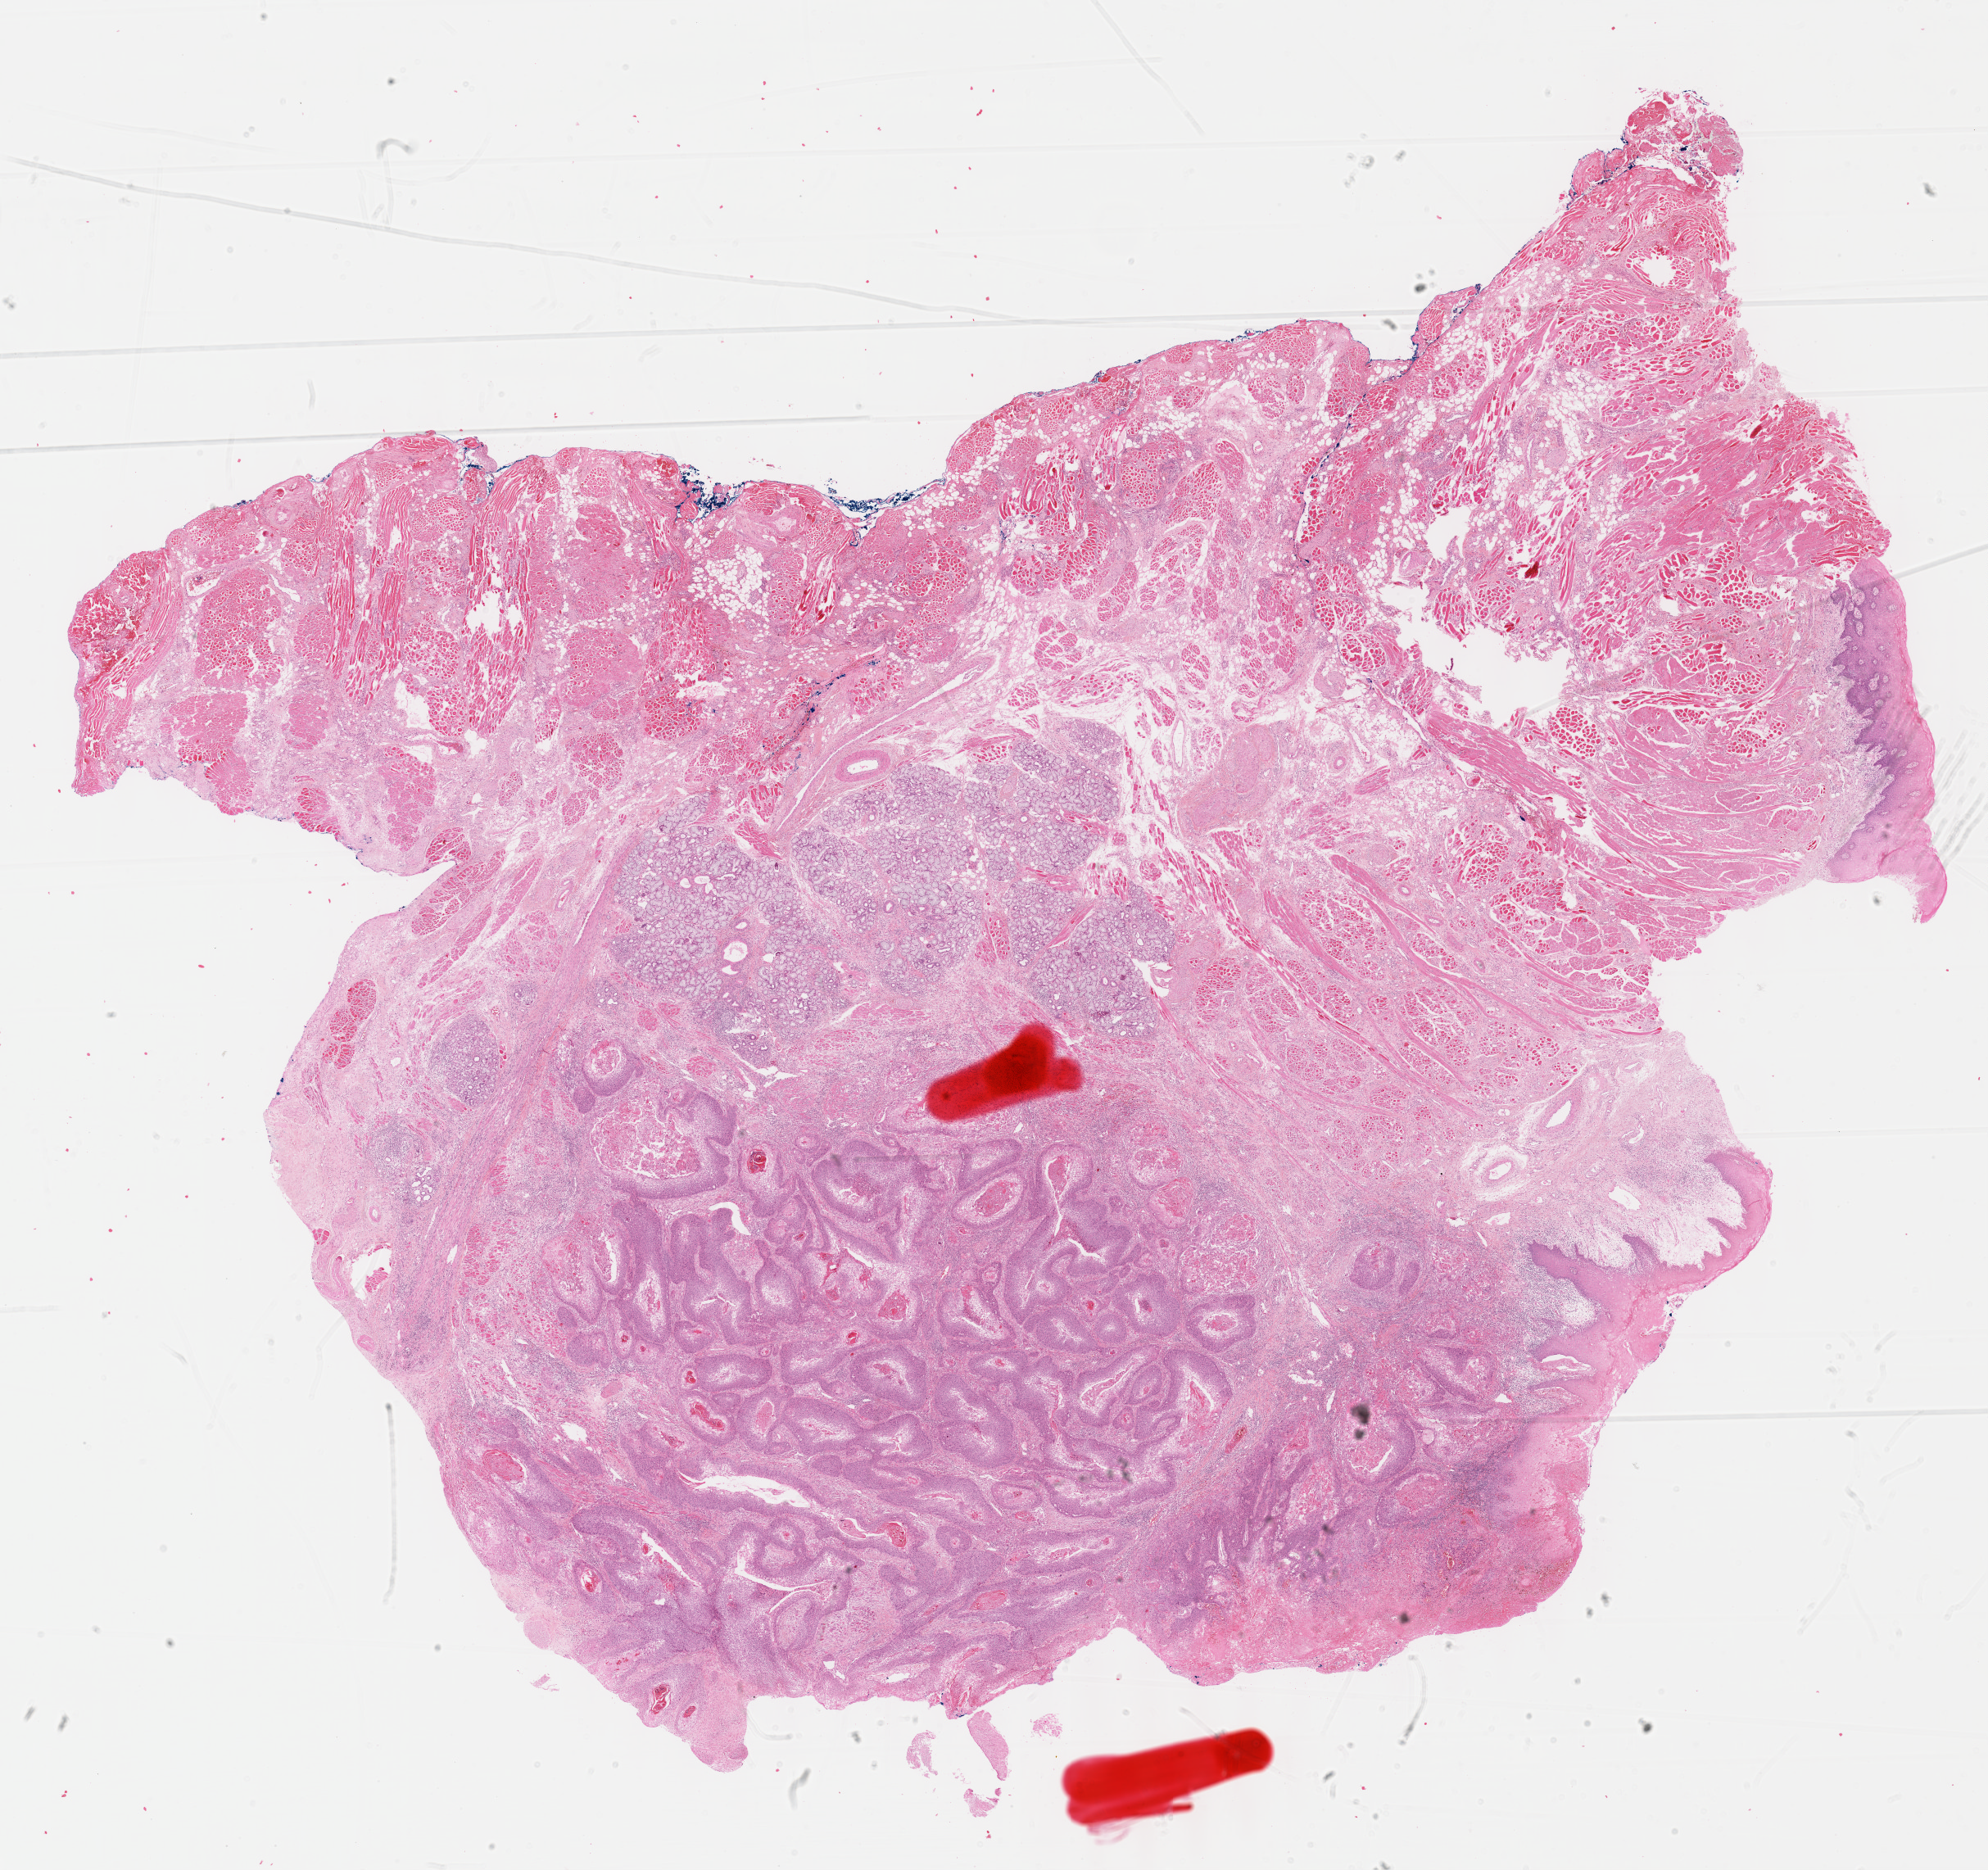
H&E whole-slide image, a low-resolution overview of the entire scanned area, about 19.6 x 18.5 mm (acquisition: 40x scan). Formalin-fixed paraffin-embedded (FFPE) diagnostic section. Primary tumour sample from the head and neck. Male patient; age at initial diagnosis 51 years. Histologic grade: G2 (moderately differentiated).
Lymph nodes positive (case pathology): 0 of 29 examined. AJCC pathologic stage: III. Pathologic diagnosis: Squamous cell carcinoma, NOS (tongue, NOS).